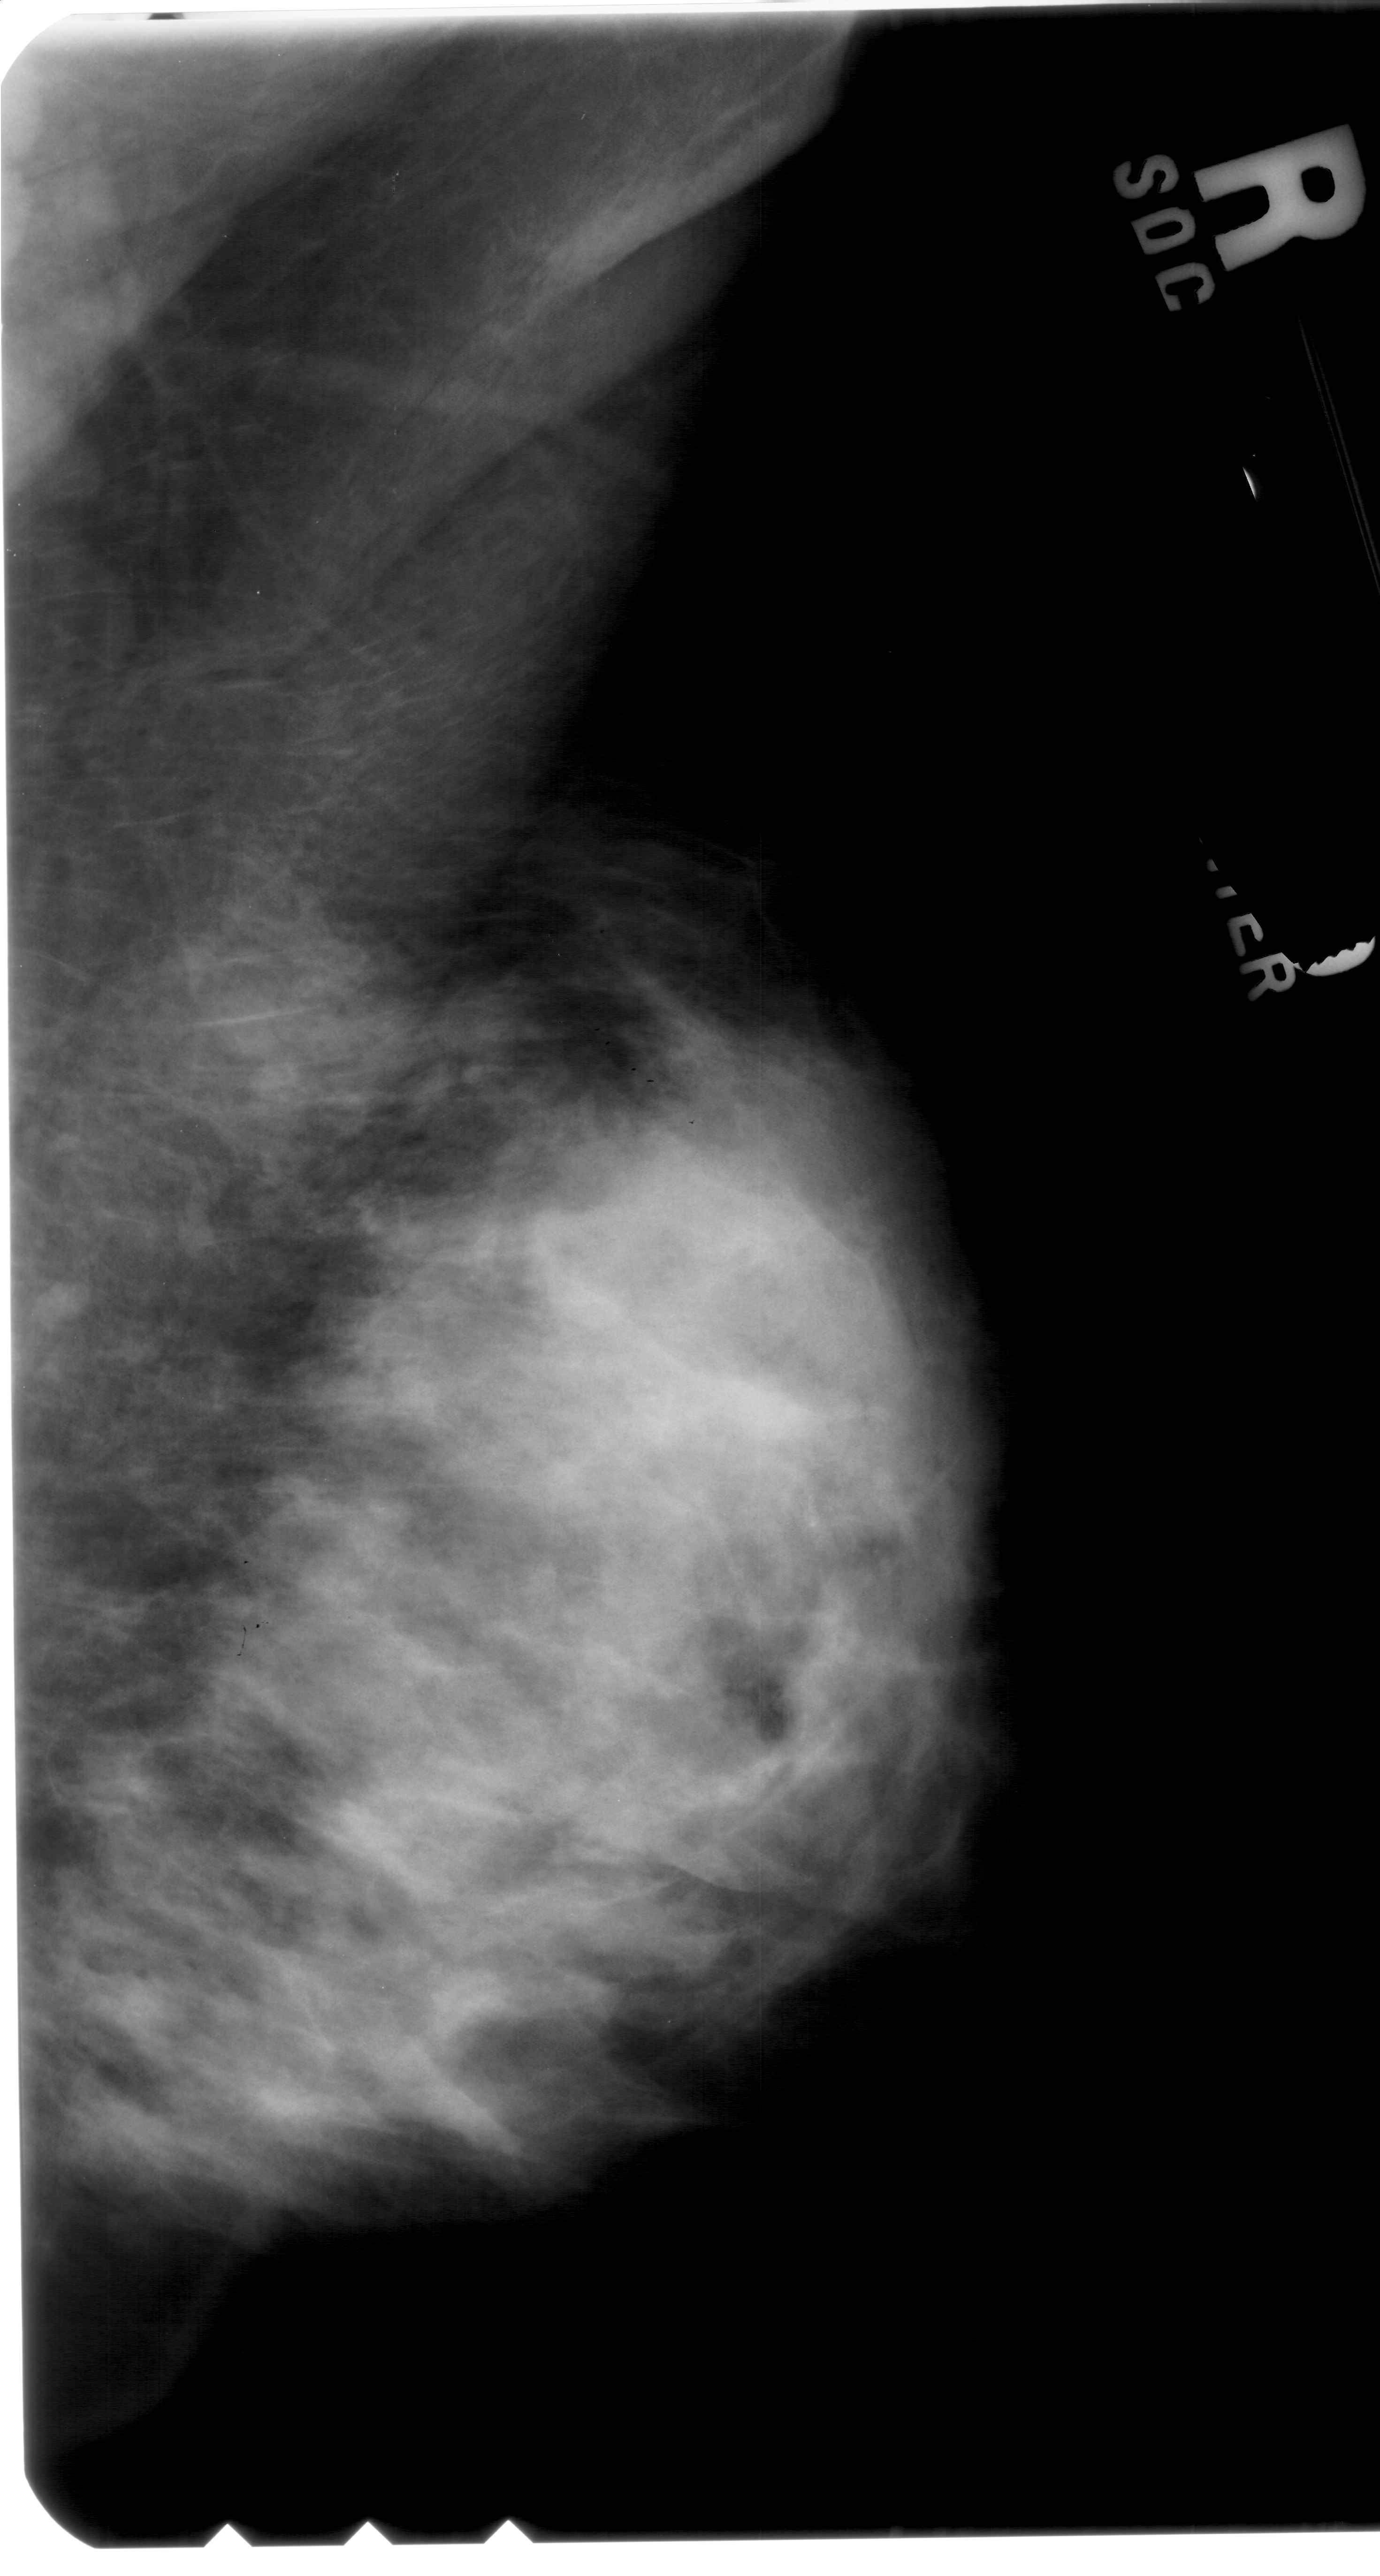
Scanned film-screen mammogram. Right breast. MLO view. BI-RADS breast density category 4 (scale 1–4). 1380 × 2576 image matrix.
Marked abnormalities (boxes around the expert regions of interest):
- calcifications, morphology punctate, distribution clustered; BI-RADS assessment category 4; subtlety rating 1 on a 1 (subtle) to 5 (obvious) scale; pathology (as recorded): benign: bounding box <782,1473,825,1530> (left, top, right, bottom; pixels)